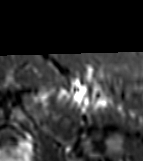
MRI of an extremity soft-tissue mass, one axial slice; slice 57 of 81 in the series (ordered by position); STIR; MR volume resampled by the dataset authors to the PET/CT grid (not the native acquisition matrix); 3.27 mm slice thickness; 143 × 161 image matrix, field of view 140 × 157 mm. Female patient. From the clinical record (not read from this slice): histological type: myxofibrosarcoma; grade: intermediate; site of the primary tumour: left thigh.
Structures marked on this image (expert contour drawn on MRI and transferred to this co-registered scan by the dataset authors):
- gross tumour volume including surrounding oedema: bounding box [x1, y1, x2, y2] px = [42, 81, 112, 107]